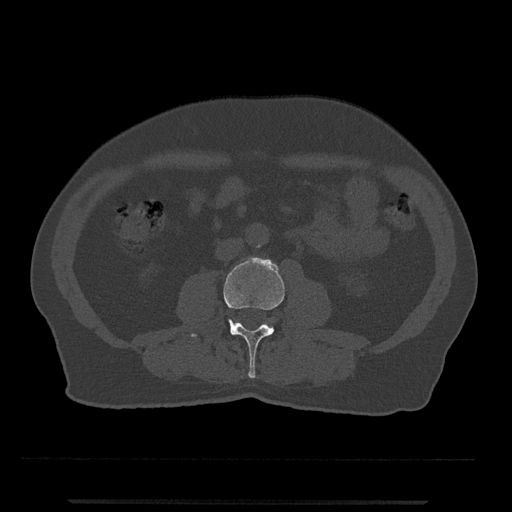
CT including the spine, one axial slice; slice 193 of 797 in the series (ordered by position); 120 kVp; bone window (W 1800 / L 400 HU); 0.5 mm slice thickness; 512 × 512 image matrix, field of view 419 × 419 mm. Patient: male, 63 years. Case-level facts recorded for this patient, not image findings: primary cancer: prostate.
Outlined on this slice (semi-automatic segmentation, software-assisted and operator-edited):
- L3 vertebra: box from (x=191, y=257) to (x=285, y=379) px